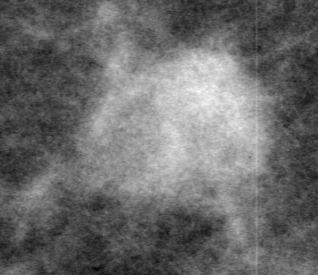
Cropped region of a digitized screen-film mammogram centred on a radiologist-marked abnormality; left breast; CC view.
Mass, shape oval, margins obscured; BI-RADS assessment category 3; pathology result (as recorded, not read from the image): malignant.